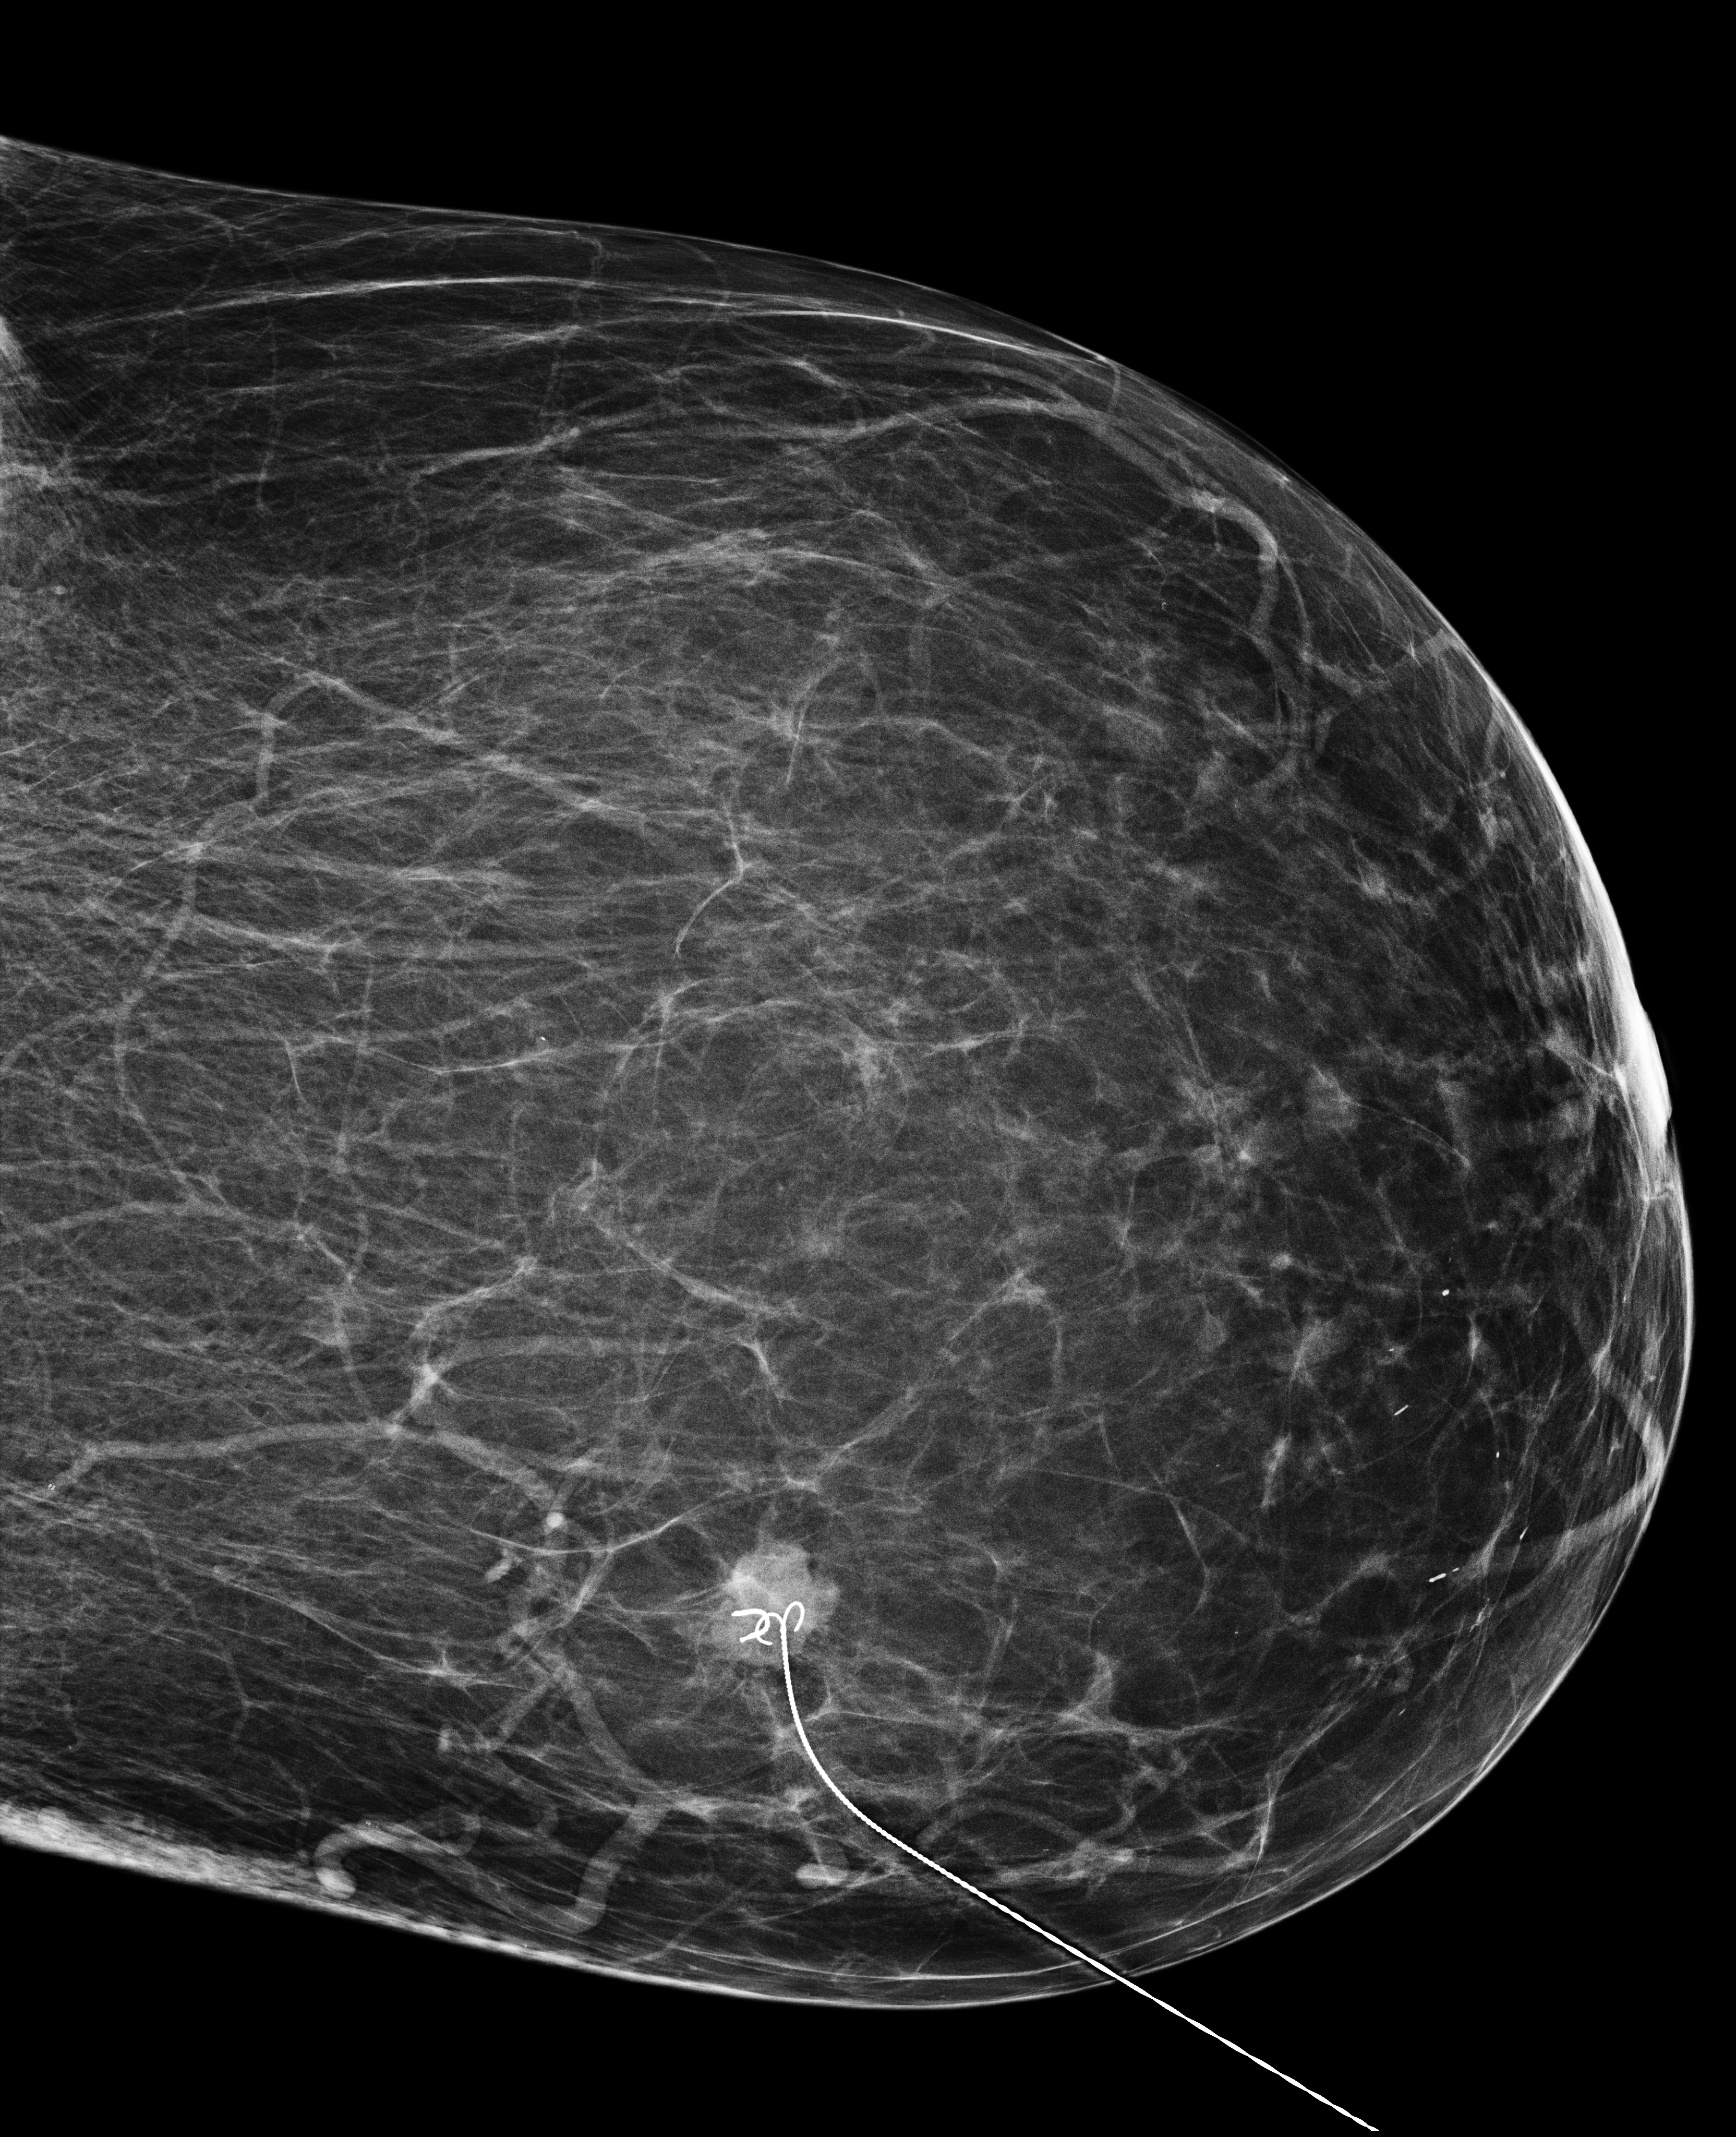
Diagnostic work-up study, compressed breast thickness 53 mm, system: Selenia Dimensions. Patient: female, 60 years.
Image type: full-field digital mammogram. Breast: left. Projection: craniocaudal (CC) view.